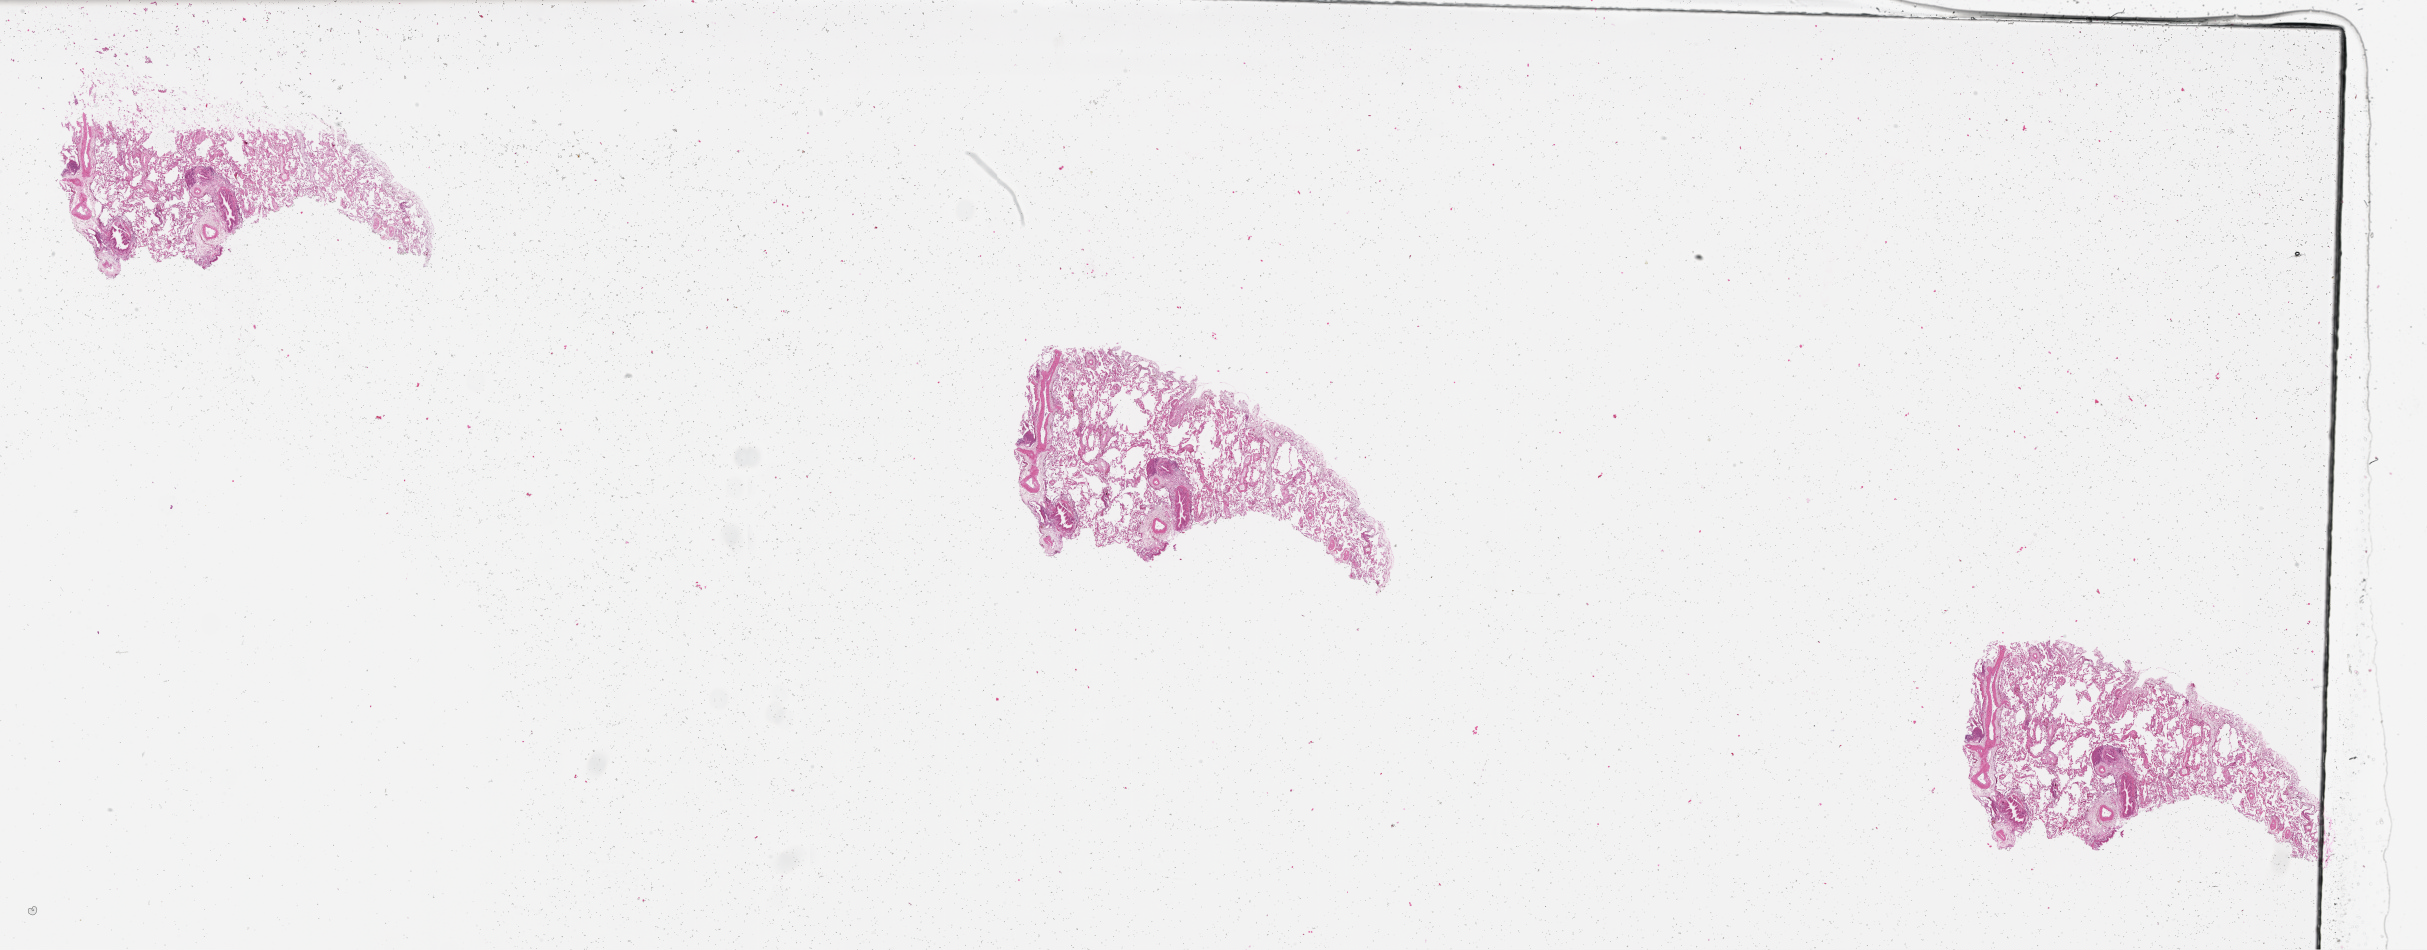
Whole-slide histology image, H&E, a low-resolution overview of the entire scanned area, about 39.1 x 15.3 mm, normal (non-tumour) tissue sample, sampled site: lung. Female, 70 y/o.
* this section: normal (non-tumour) tissue from the same patient
* patient diagnosis: Adenocarcinoma, NOS